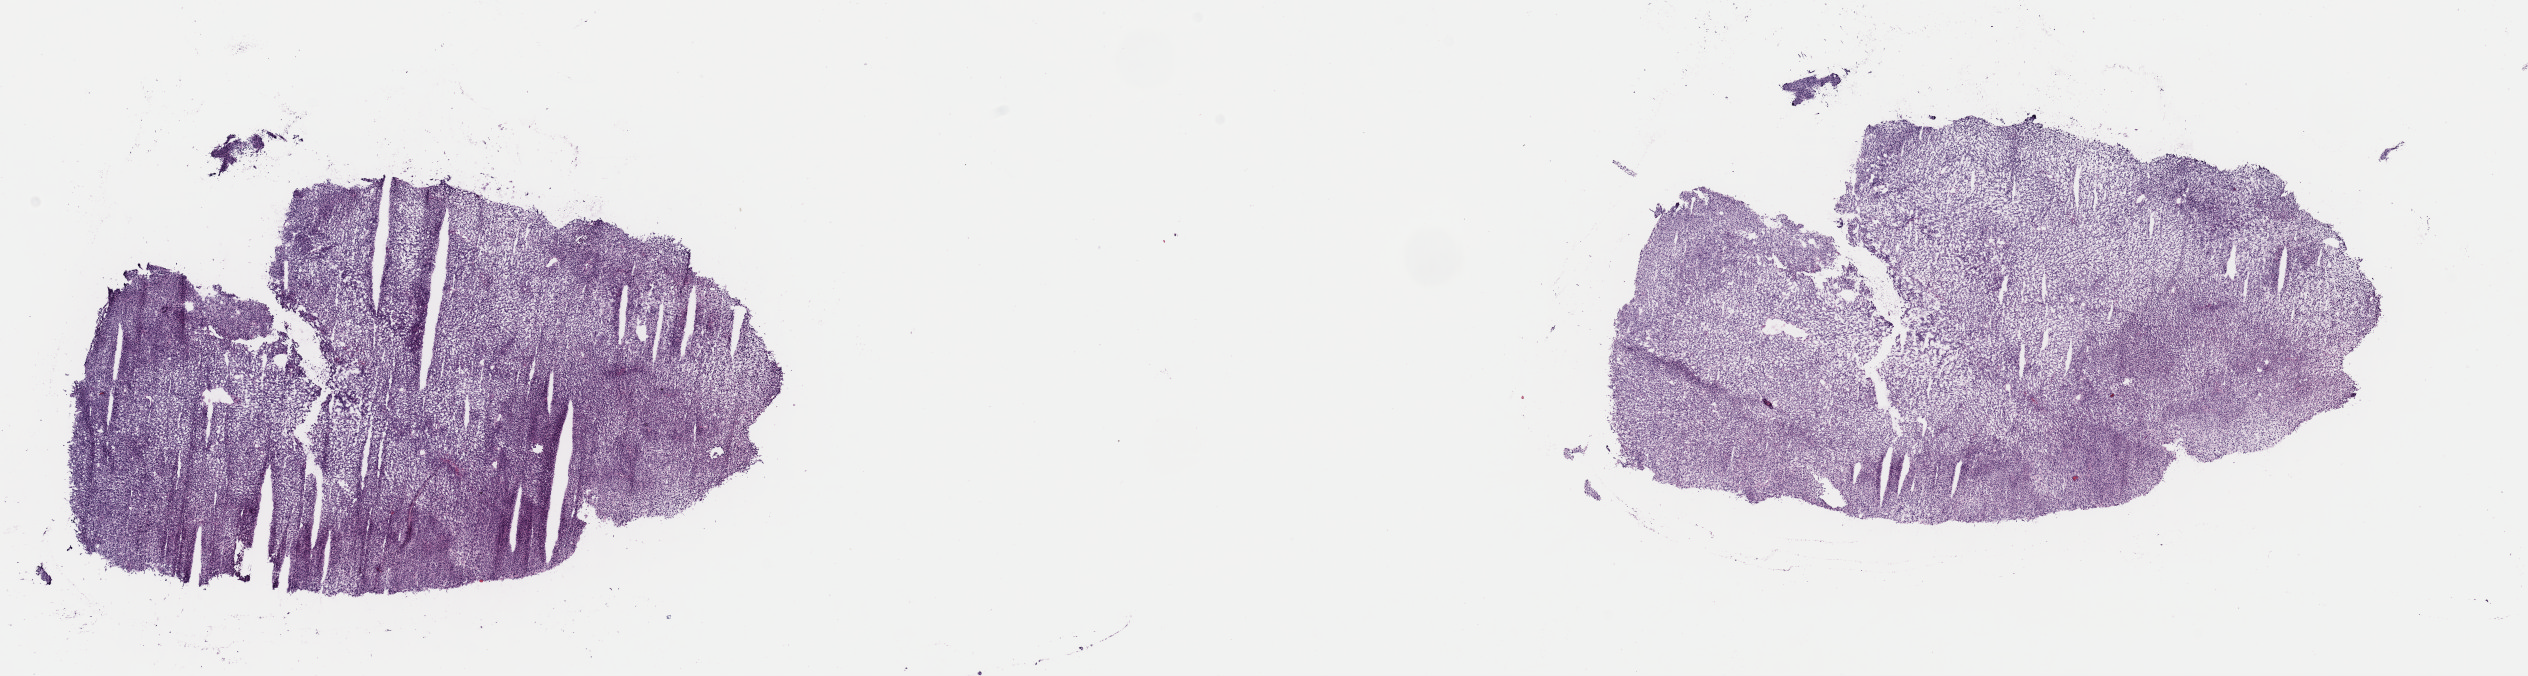
H&E-stained whole-slide image, a low-resolution overview of the entire scanned area, about 20.0 x 5.3 mm (slide scanned at 40x). Frozen section. Sample: primary tumour, uterus. Patient: female, age at initial diagnosis 43 years. Pathologist review of this section (percent, as recorded): tumour cells 100%, tumour nuclei 85%, normal cells 0%, stromal cells 0%, necrosis 0%. Infiltration values recorded for this section: lymphocyte infiltration 1%, monocyte infiltration 0%, neutrophil infiltration 0%.
• diagnosis: Leiomyosarcoma, NOS